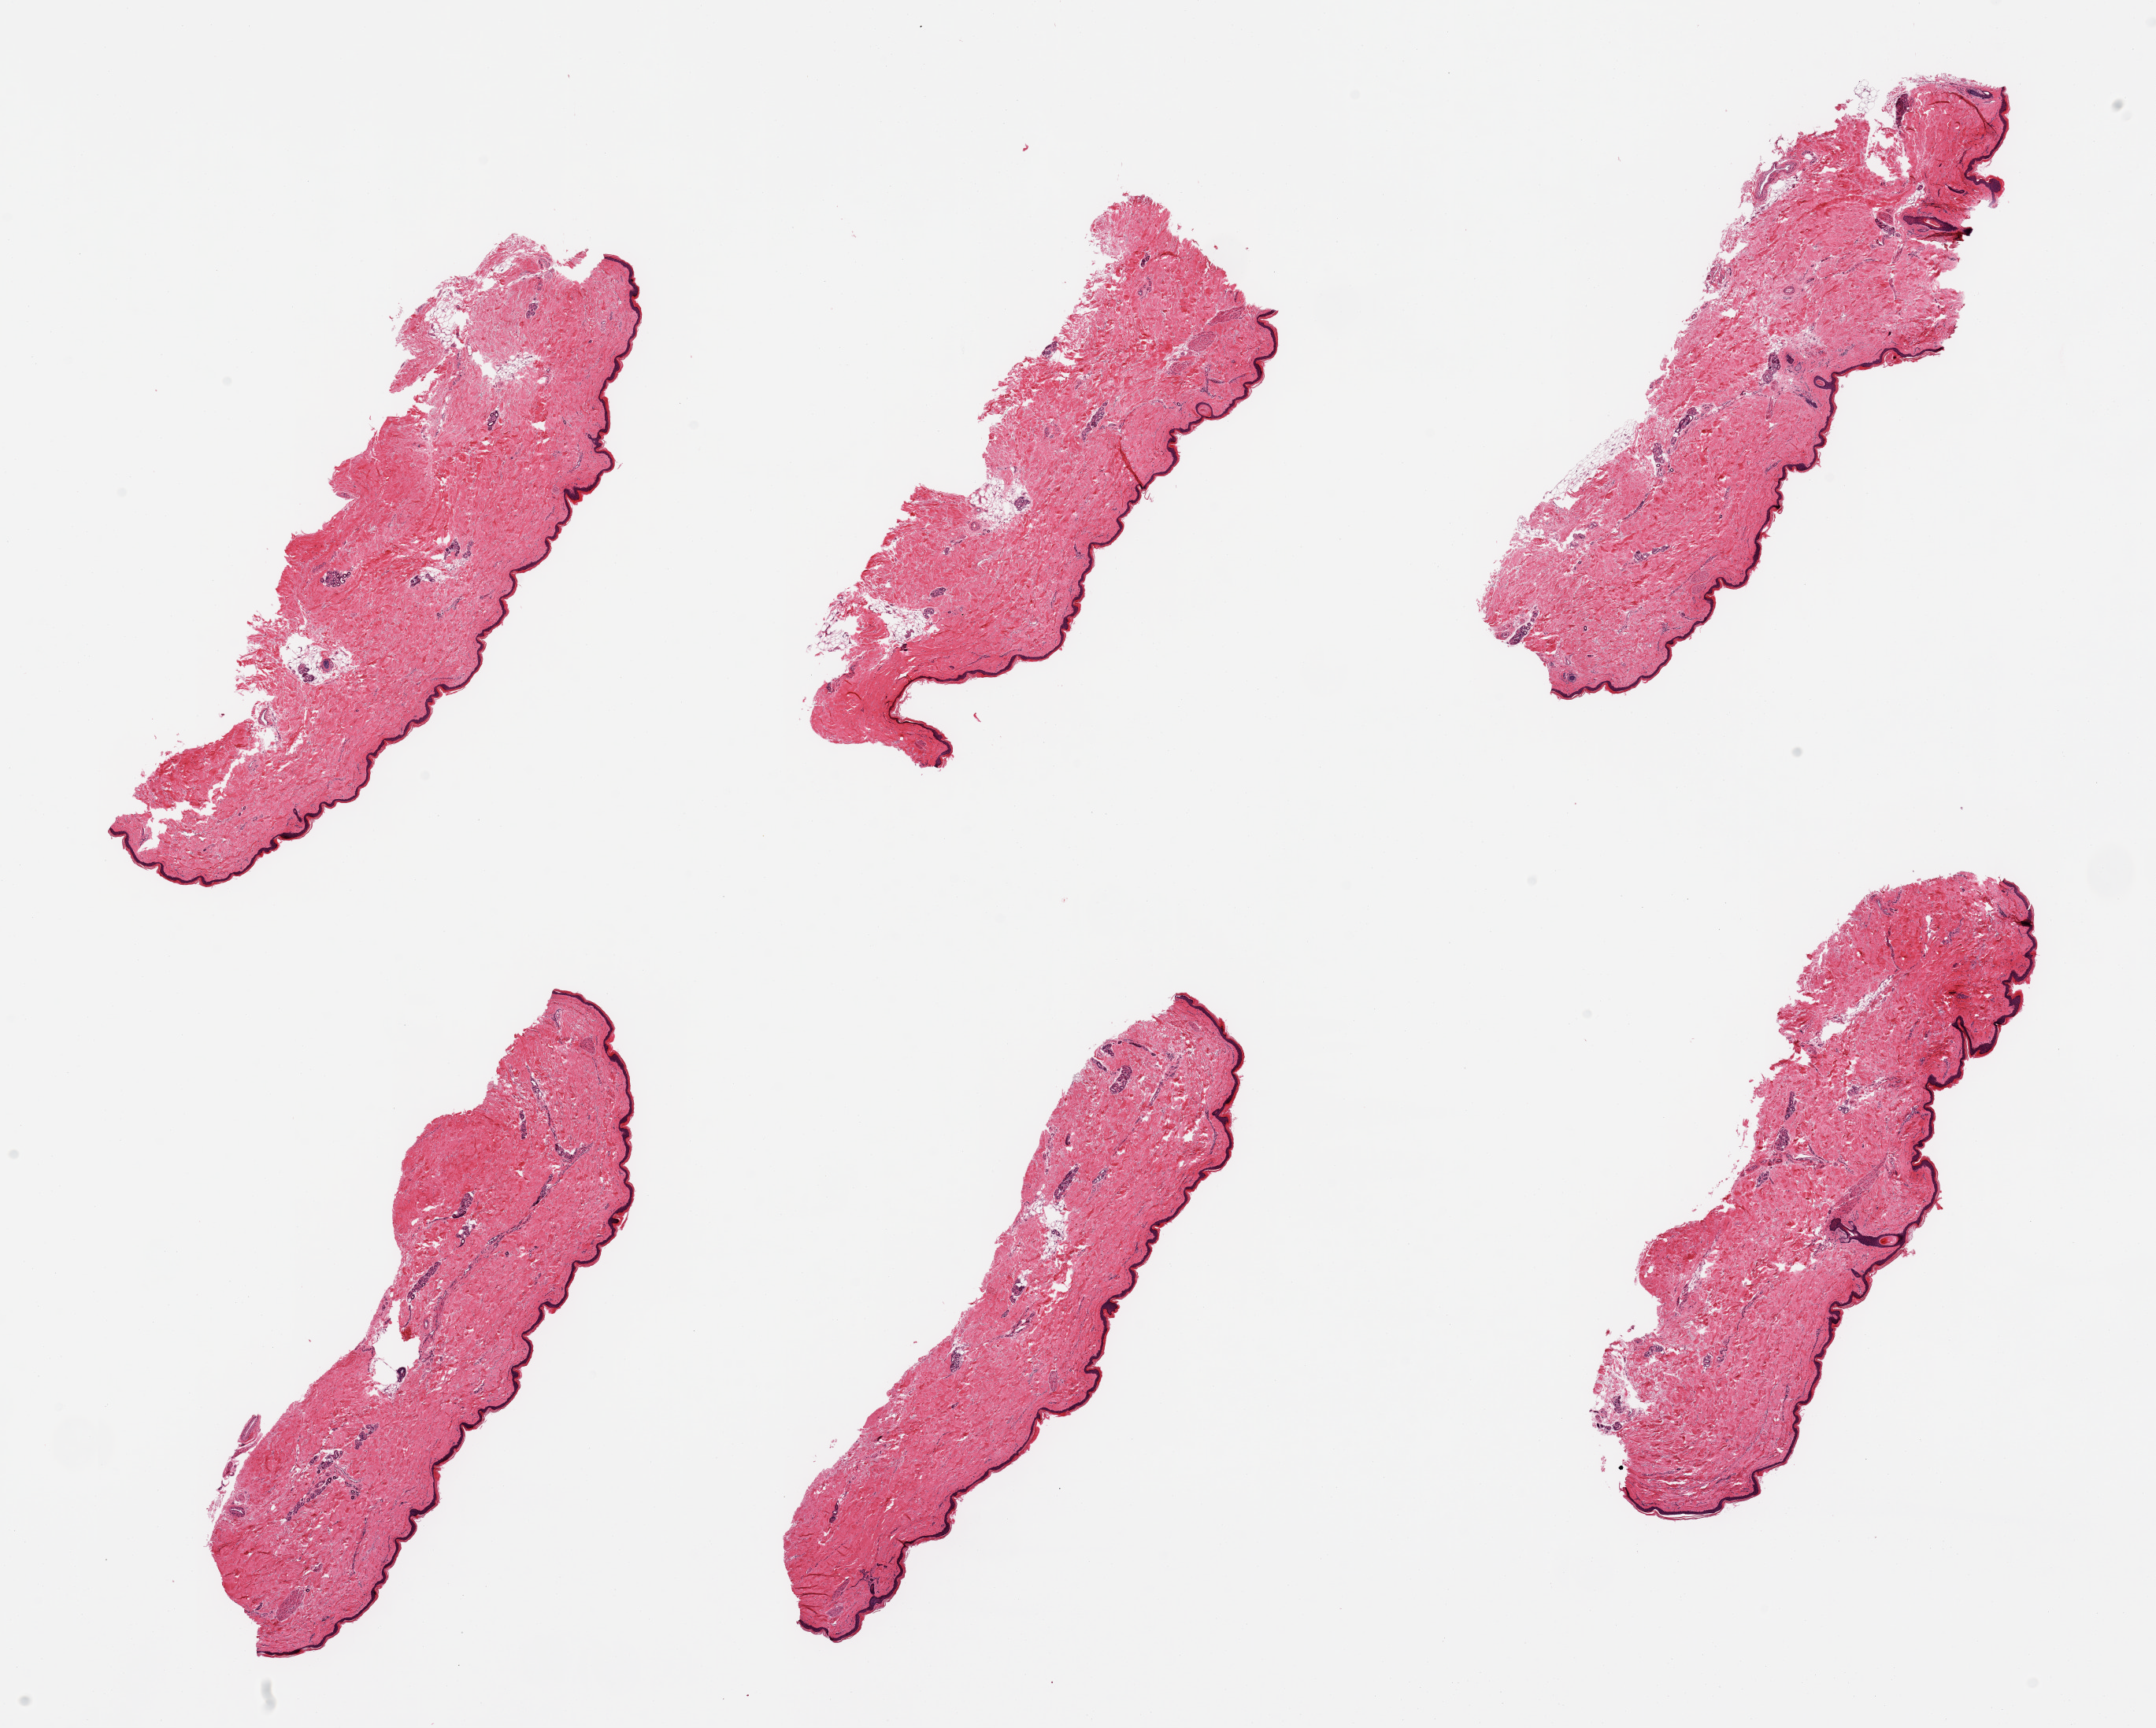
Haematoxylin and eosin whole-slide image — whole scanned area (about 21.7 x 17.4 mm, acquisition: 20x scan) shown as a low-resolution overview; PAXgene-fixed, paraffin-embedded tissue; section of skin of lower leg (target tissue); donor tissue sample. Donor sex: female.
Pathologist's review note for this sample: 6 pieces; well trimmed; <5% dermal fat.